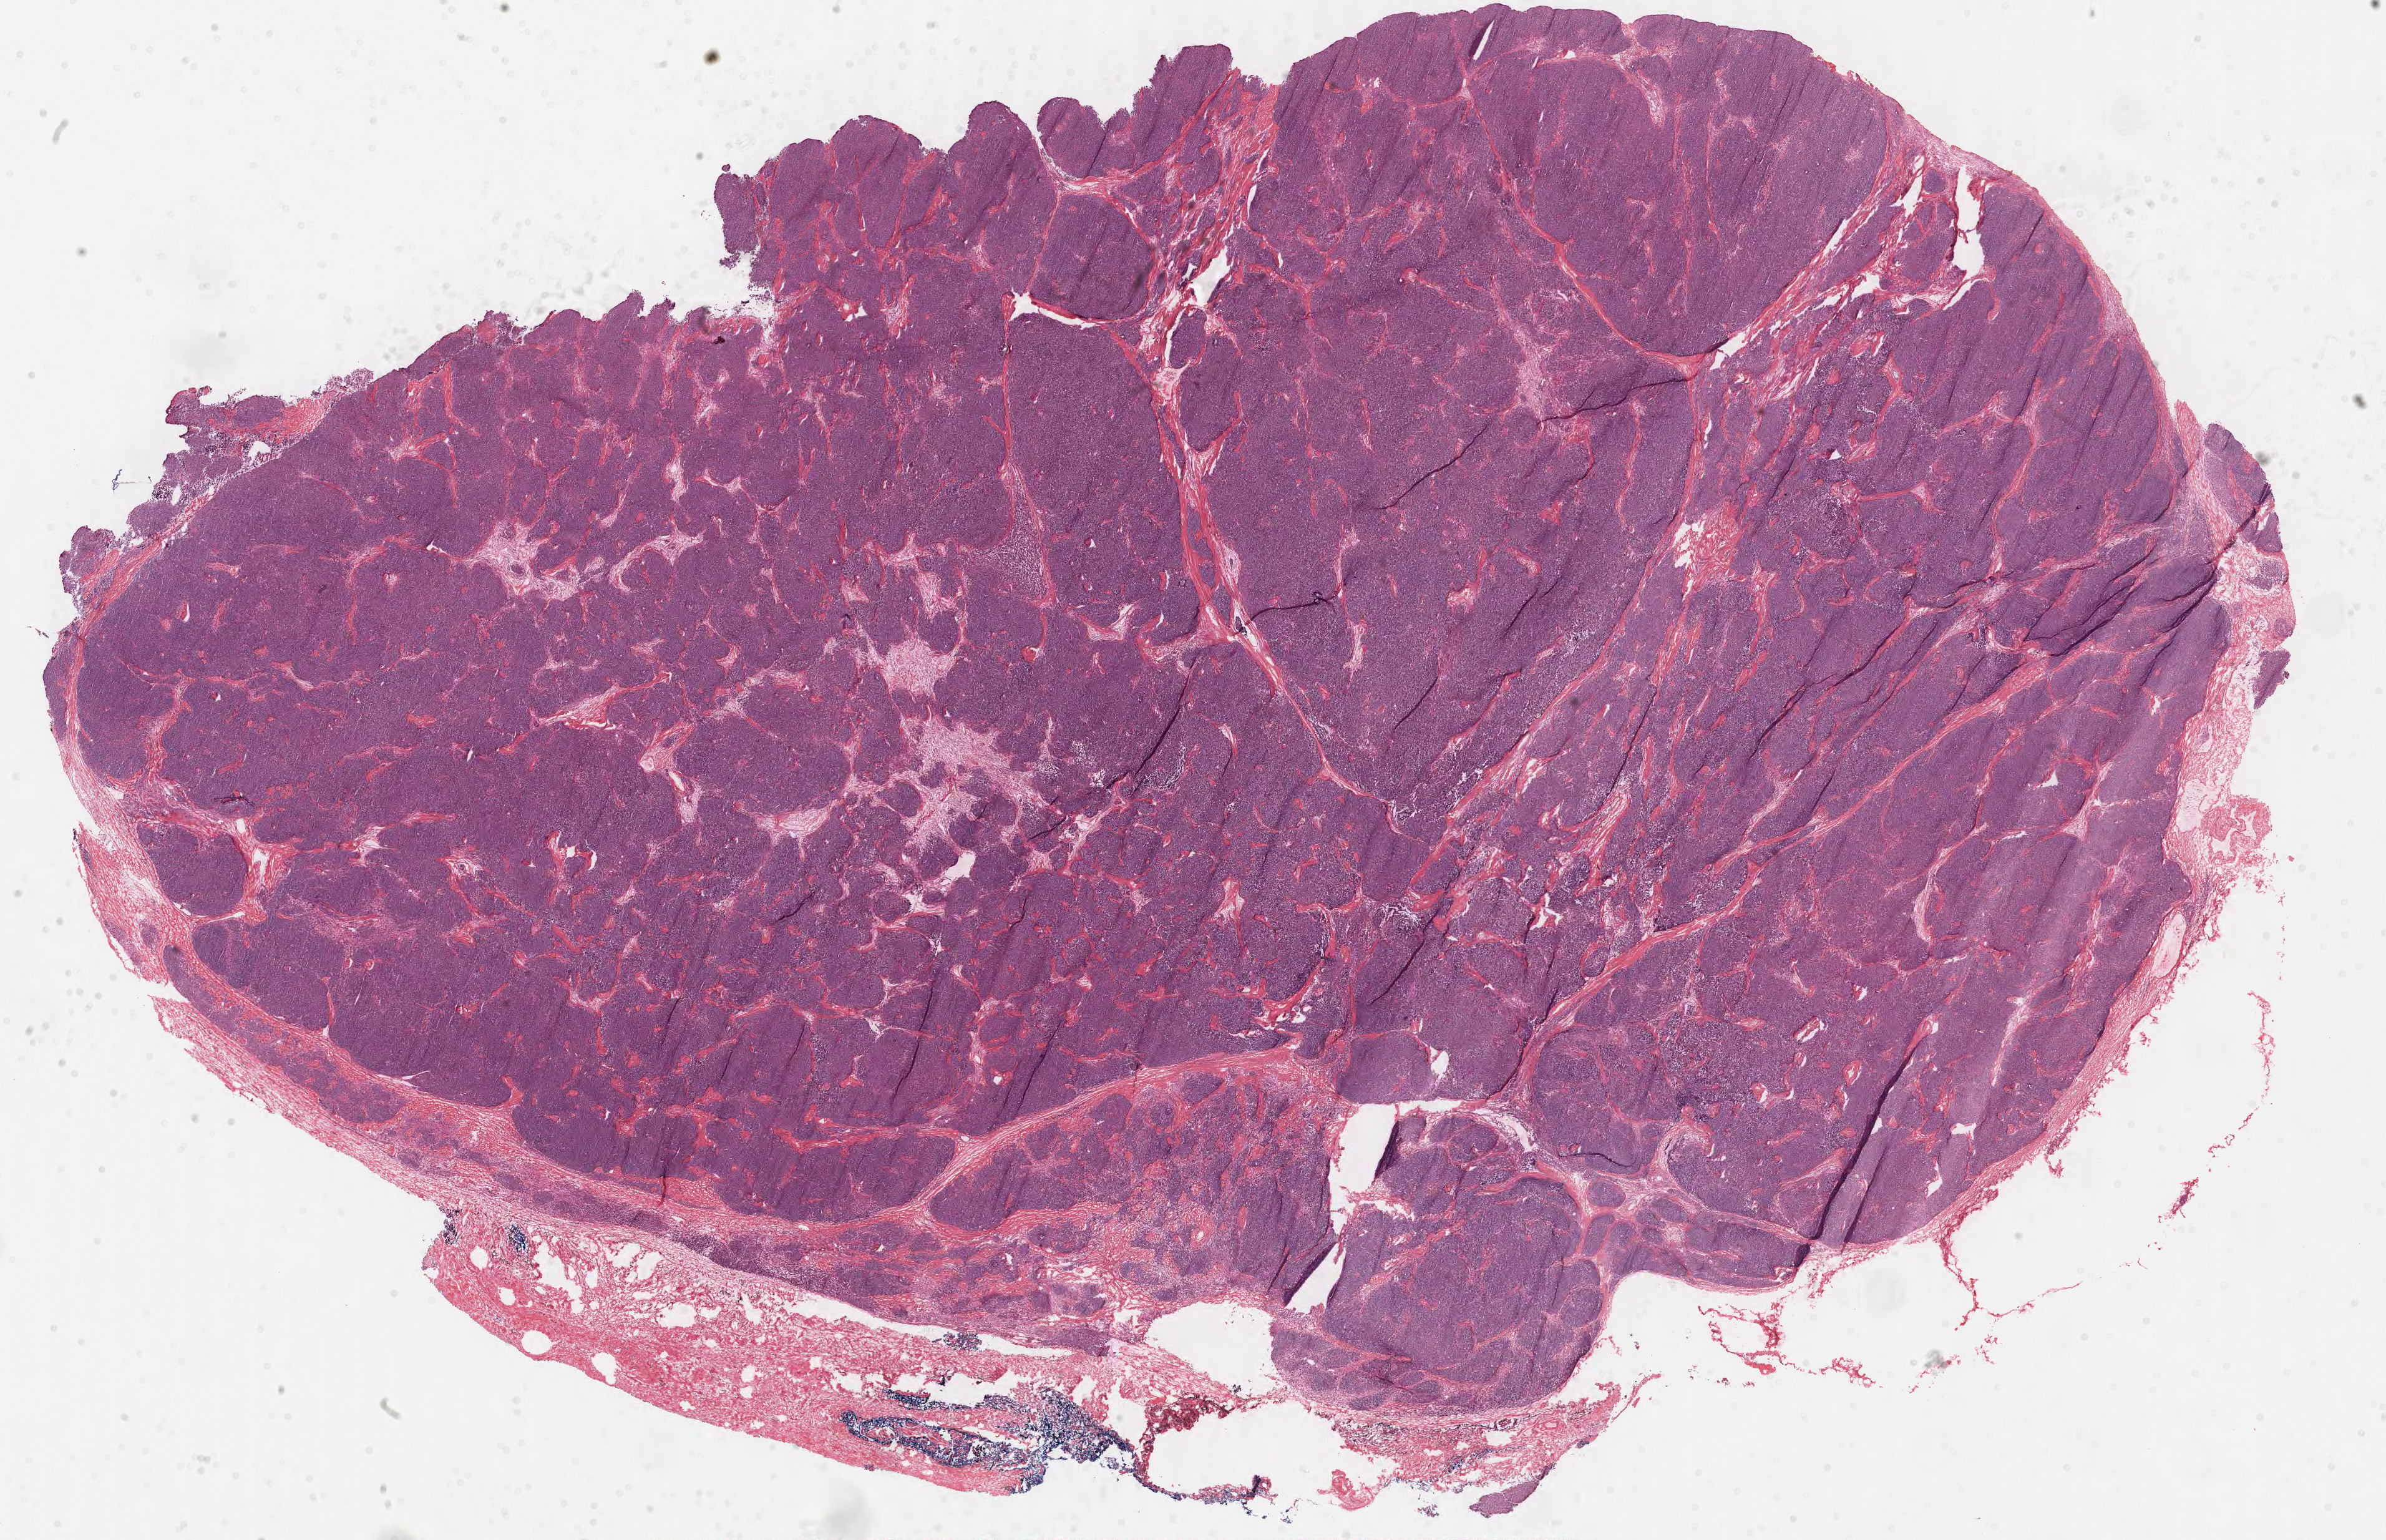
H&E-stained whole-slide image — whole scanned area (about 30.3 x 19.6 mm, acquisition: 40x scan) shown as a low-resolution overview; formalin-fixed paraffin-embedded (FFPE) diagnostic section; primary tumour sample from the thymus. Female, age 50 years at initial diagnosis.
Histologic diagnosis: Thymoma, type AB, malignant.